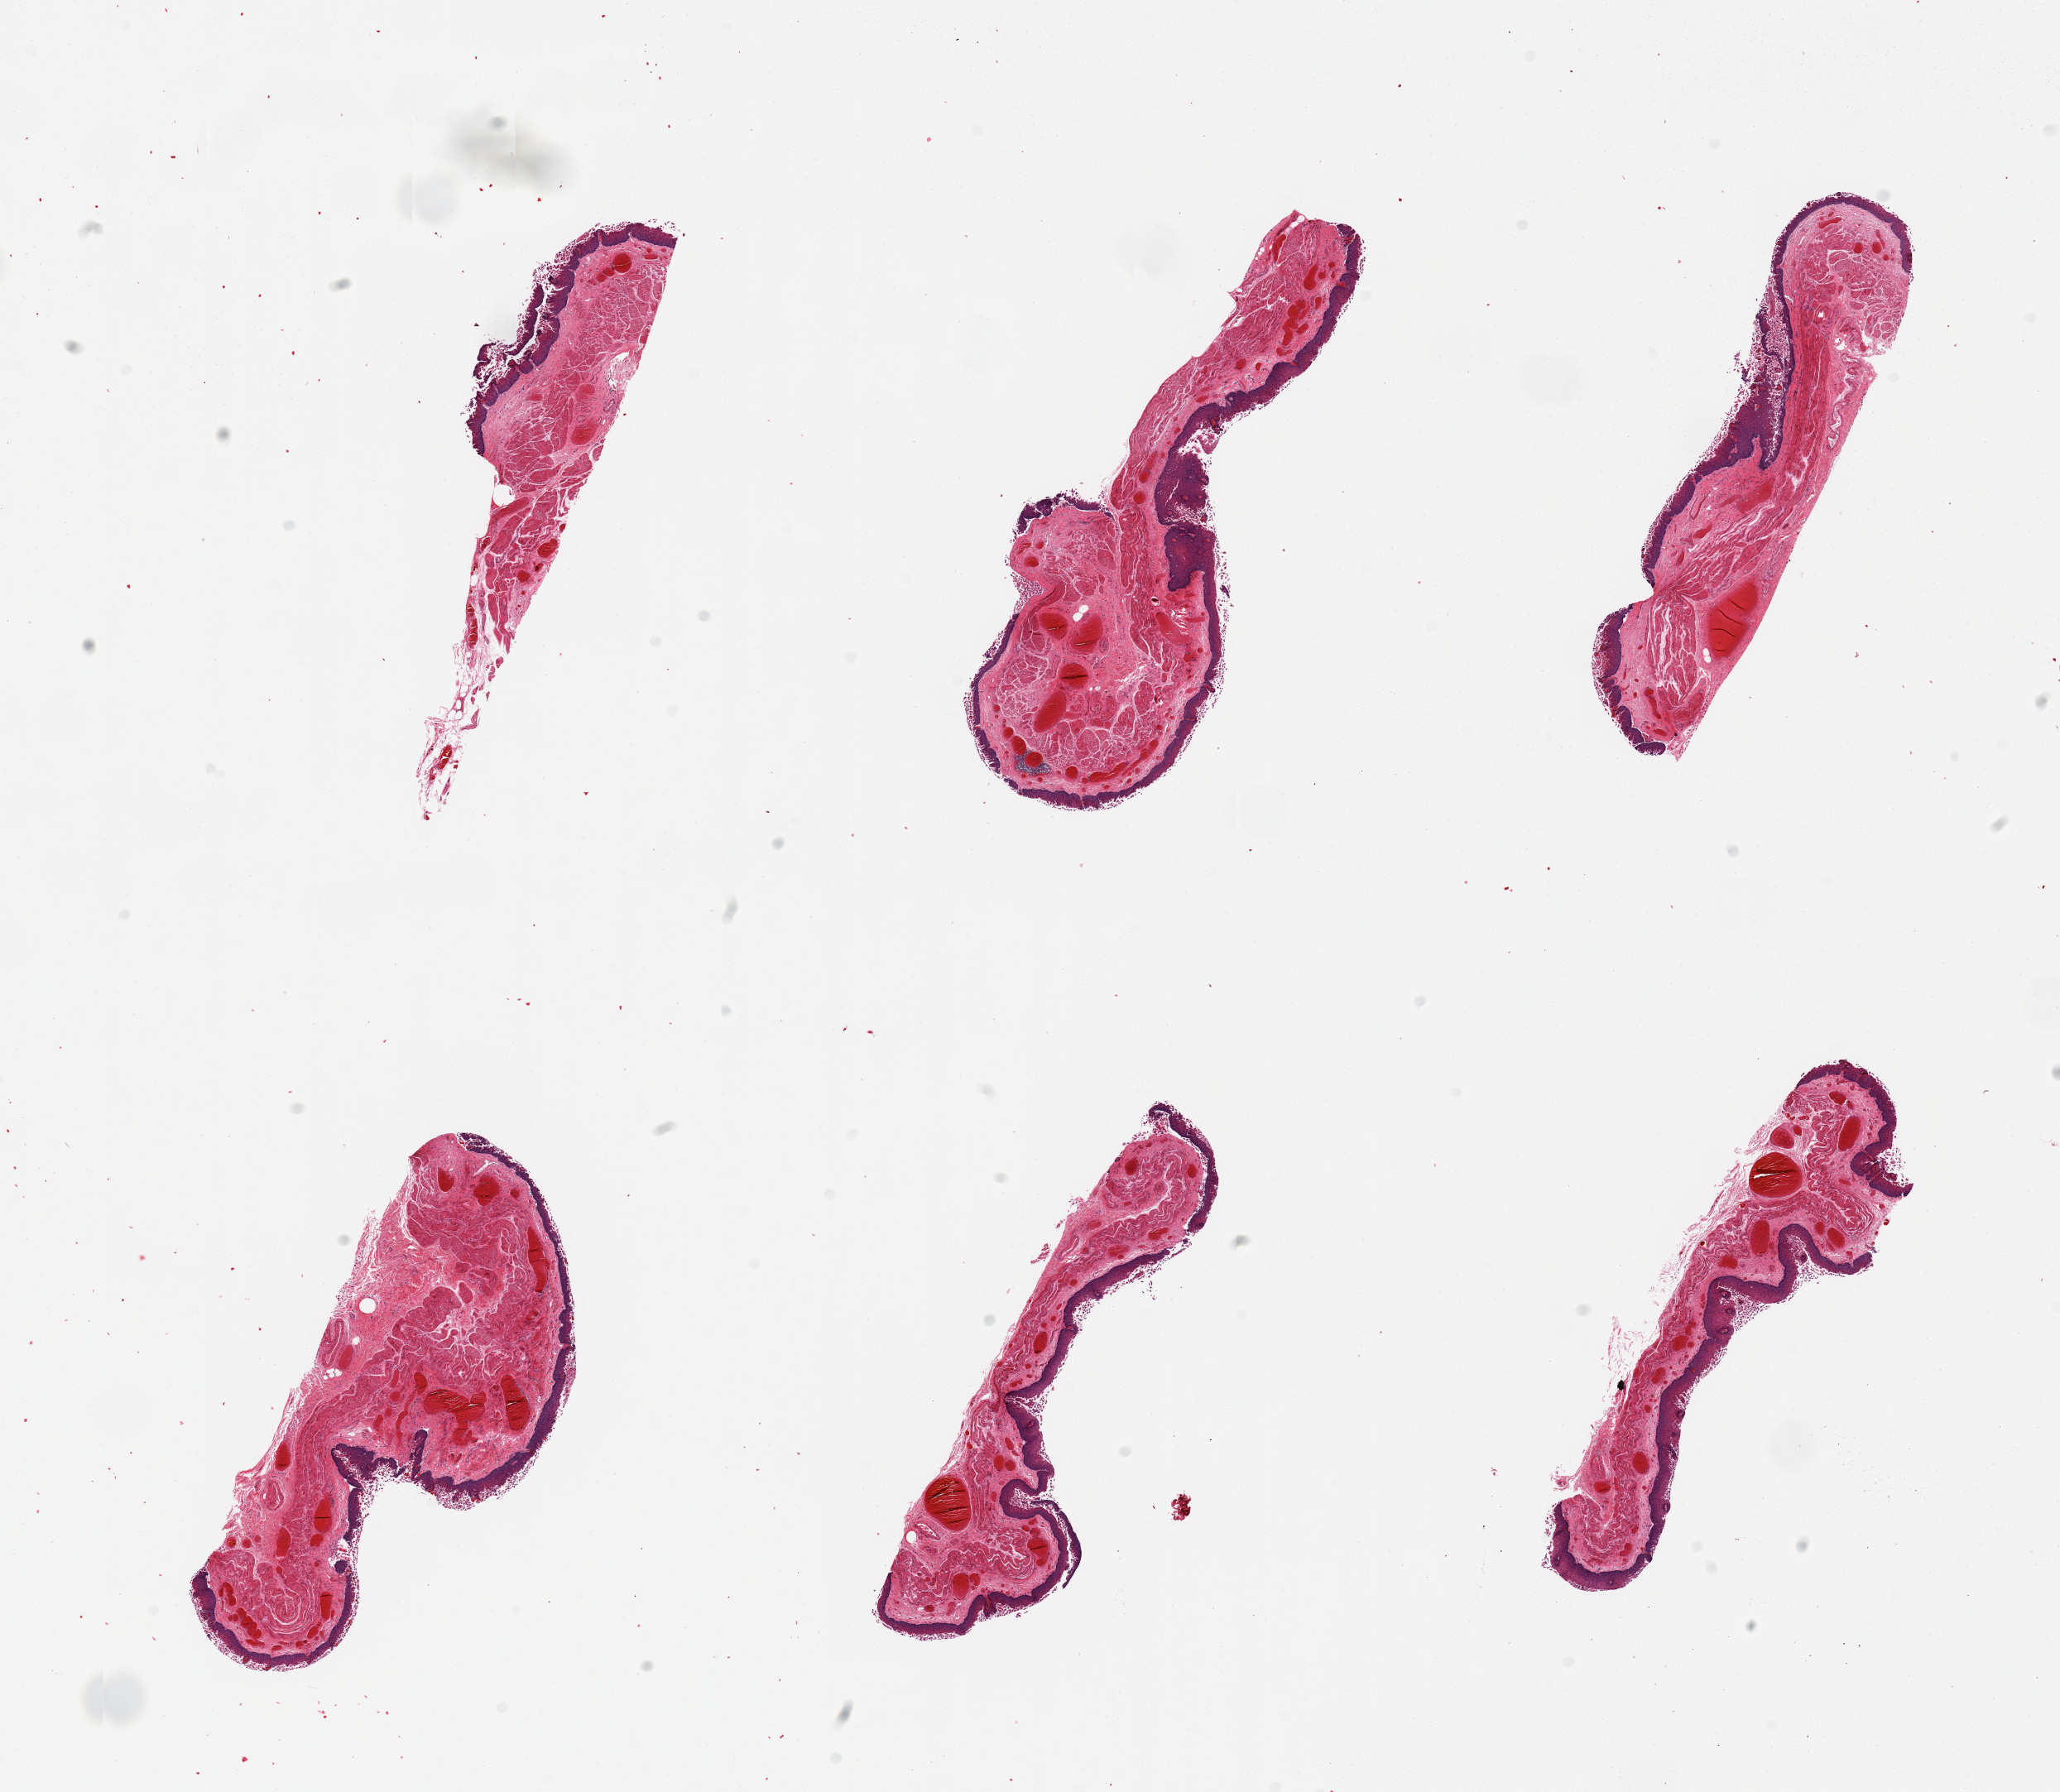
Digitized haematoxylin and eosin-stained section — a low-resolution overview of the entire scanned area, about 19.7 x 17.1 mm, PAXgene-fixed paraffin-embedded (PFPE) section, target tissue: esophageal mucous membrane, donor tissue sample. Male donor.
Review note (as recorded): 6 pieces, squamous mucosa is ~10% thickness, beginning to slough, autolysis score is '2' in some areas.